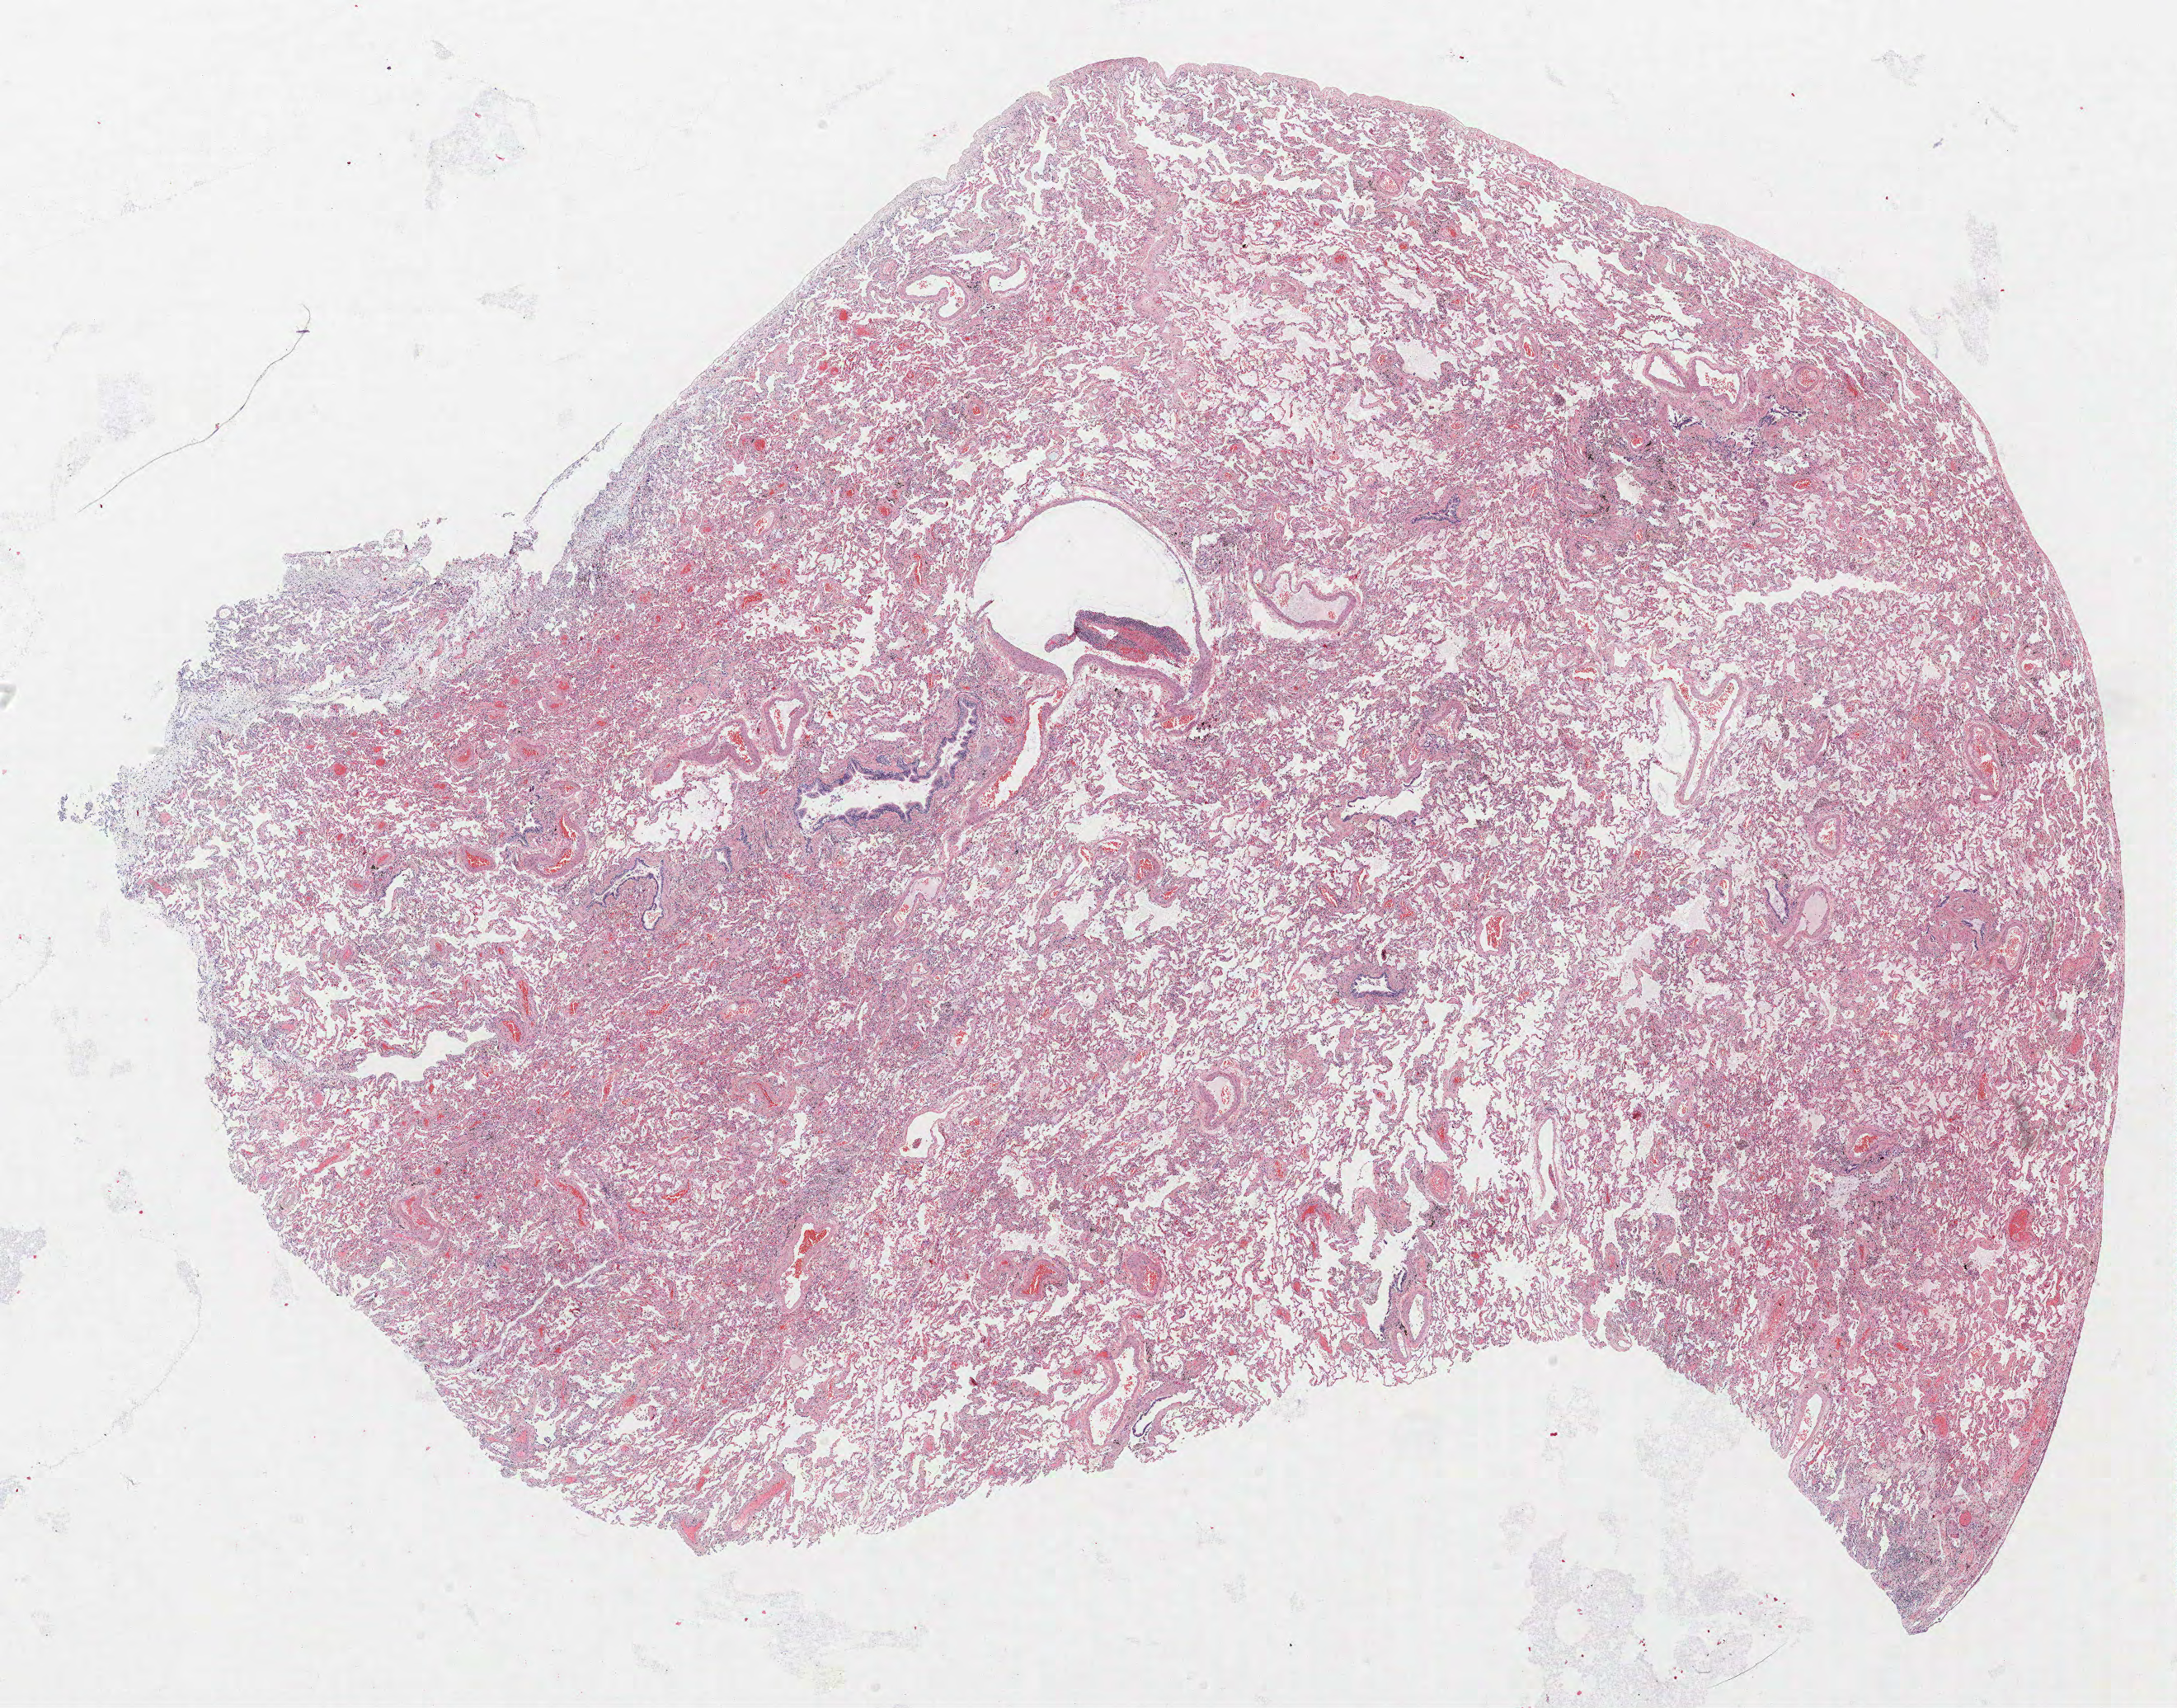
Whole-slide histology image, Hematoxylin and eosin (H&E) stained, a low-resolution overview of the entire scanned area, about 21.1 x 16.6 mm (slide scanned at 40x), formalin-fixed paraffin-embedded (FFPE) section, lung tissue. Female, age 56 at enrolment. Grade: poorly differentiated (G3).
* stage (AJCC 6th edition): IIB
* participant's lung-cancer diagnosis: Adenocarcinoma, NOS
* primary tumour location (clinical record): right lower lobe
* tumour size (pathology): 60 mm